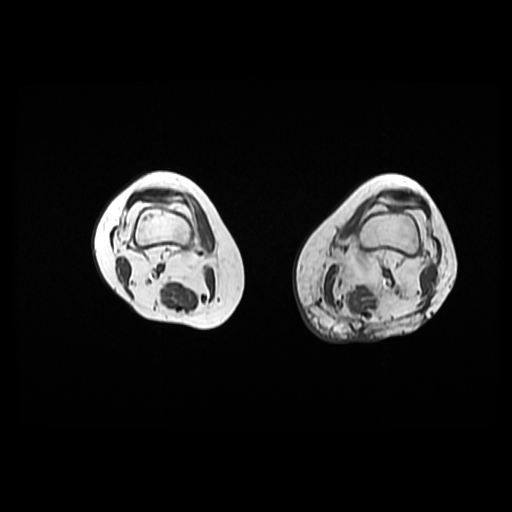
MRI of an extremity soft-tissue mass, one axial slice; position 13 of 42 along the scan axis; 6 mm slice thickness; 512 × 512 image matrix, field of view 420 × 420 mm. Female patient. Case-level facts recorded for this patient, not image findings: histological type: pleomorphic leiomyosarcoma; grade: high; site of the primary tumour: left thigh.
Outlined on this slice (outlined manually by an expert reader):
- gross tumour volume including surrounding oedema: bounding box (x1, y1, x2, y2) in pixels: (316, 266, 344, 314)